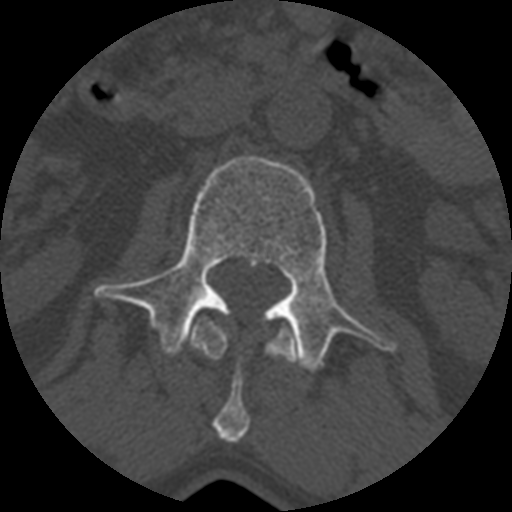
CT including the spine, one axial slice. Position 339 of 399 along the scan axis. 120 kVp. Bone window (W 1800 / L 400 HU). 1.25 mm slice thickness. 512 × 512 image matrix, field of view 160 × 160 mm. Patient age 71 years. From the clinical record (not read from this slice): primary cancer: prostate.
Annotated regions visible in this slice (semi-automatic segmentation, software-assisted and operator-edited):
- L1 vertebra: bounding box <190,313,296,441> (left, top, right, bottom; pixels)
- L2 vertebra: <95,156,397,374>